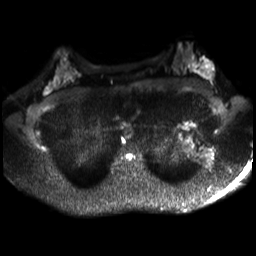
Breast MRI, one axial slice; diffusion-weighted series; image 2 of 4 stored at this slice position (different b-values; order by instance number); 3 T; 4 mm slice thickness; 256 × 256 image matrix, field of view 320 × 320 mm. Female patient.
Structures marked on this image (expert manual segmentation):
- tumour on diffusion-weighted imaging: bounding box <203,62,211,75> (left, top, right, bottom; pixels)